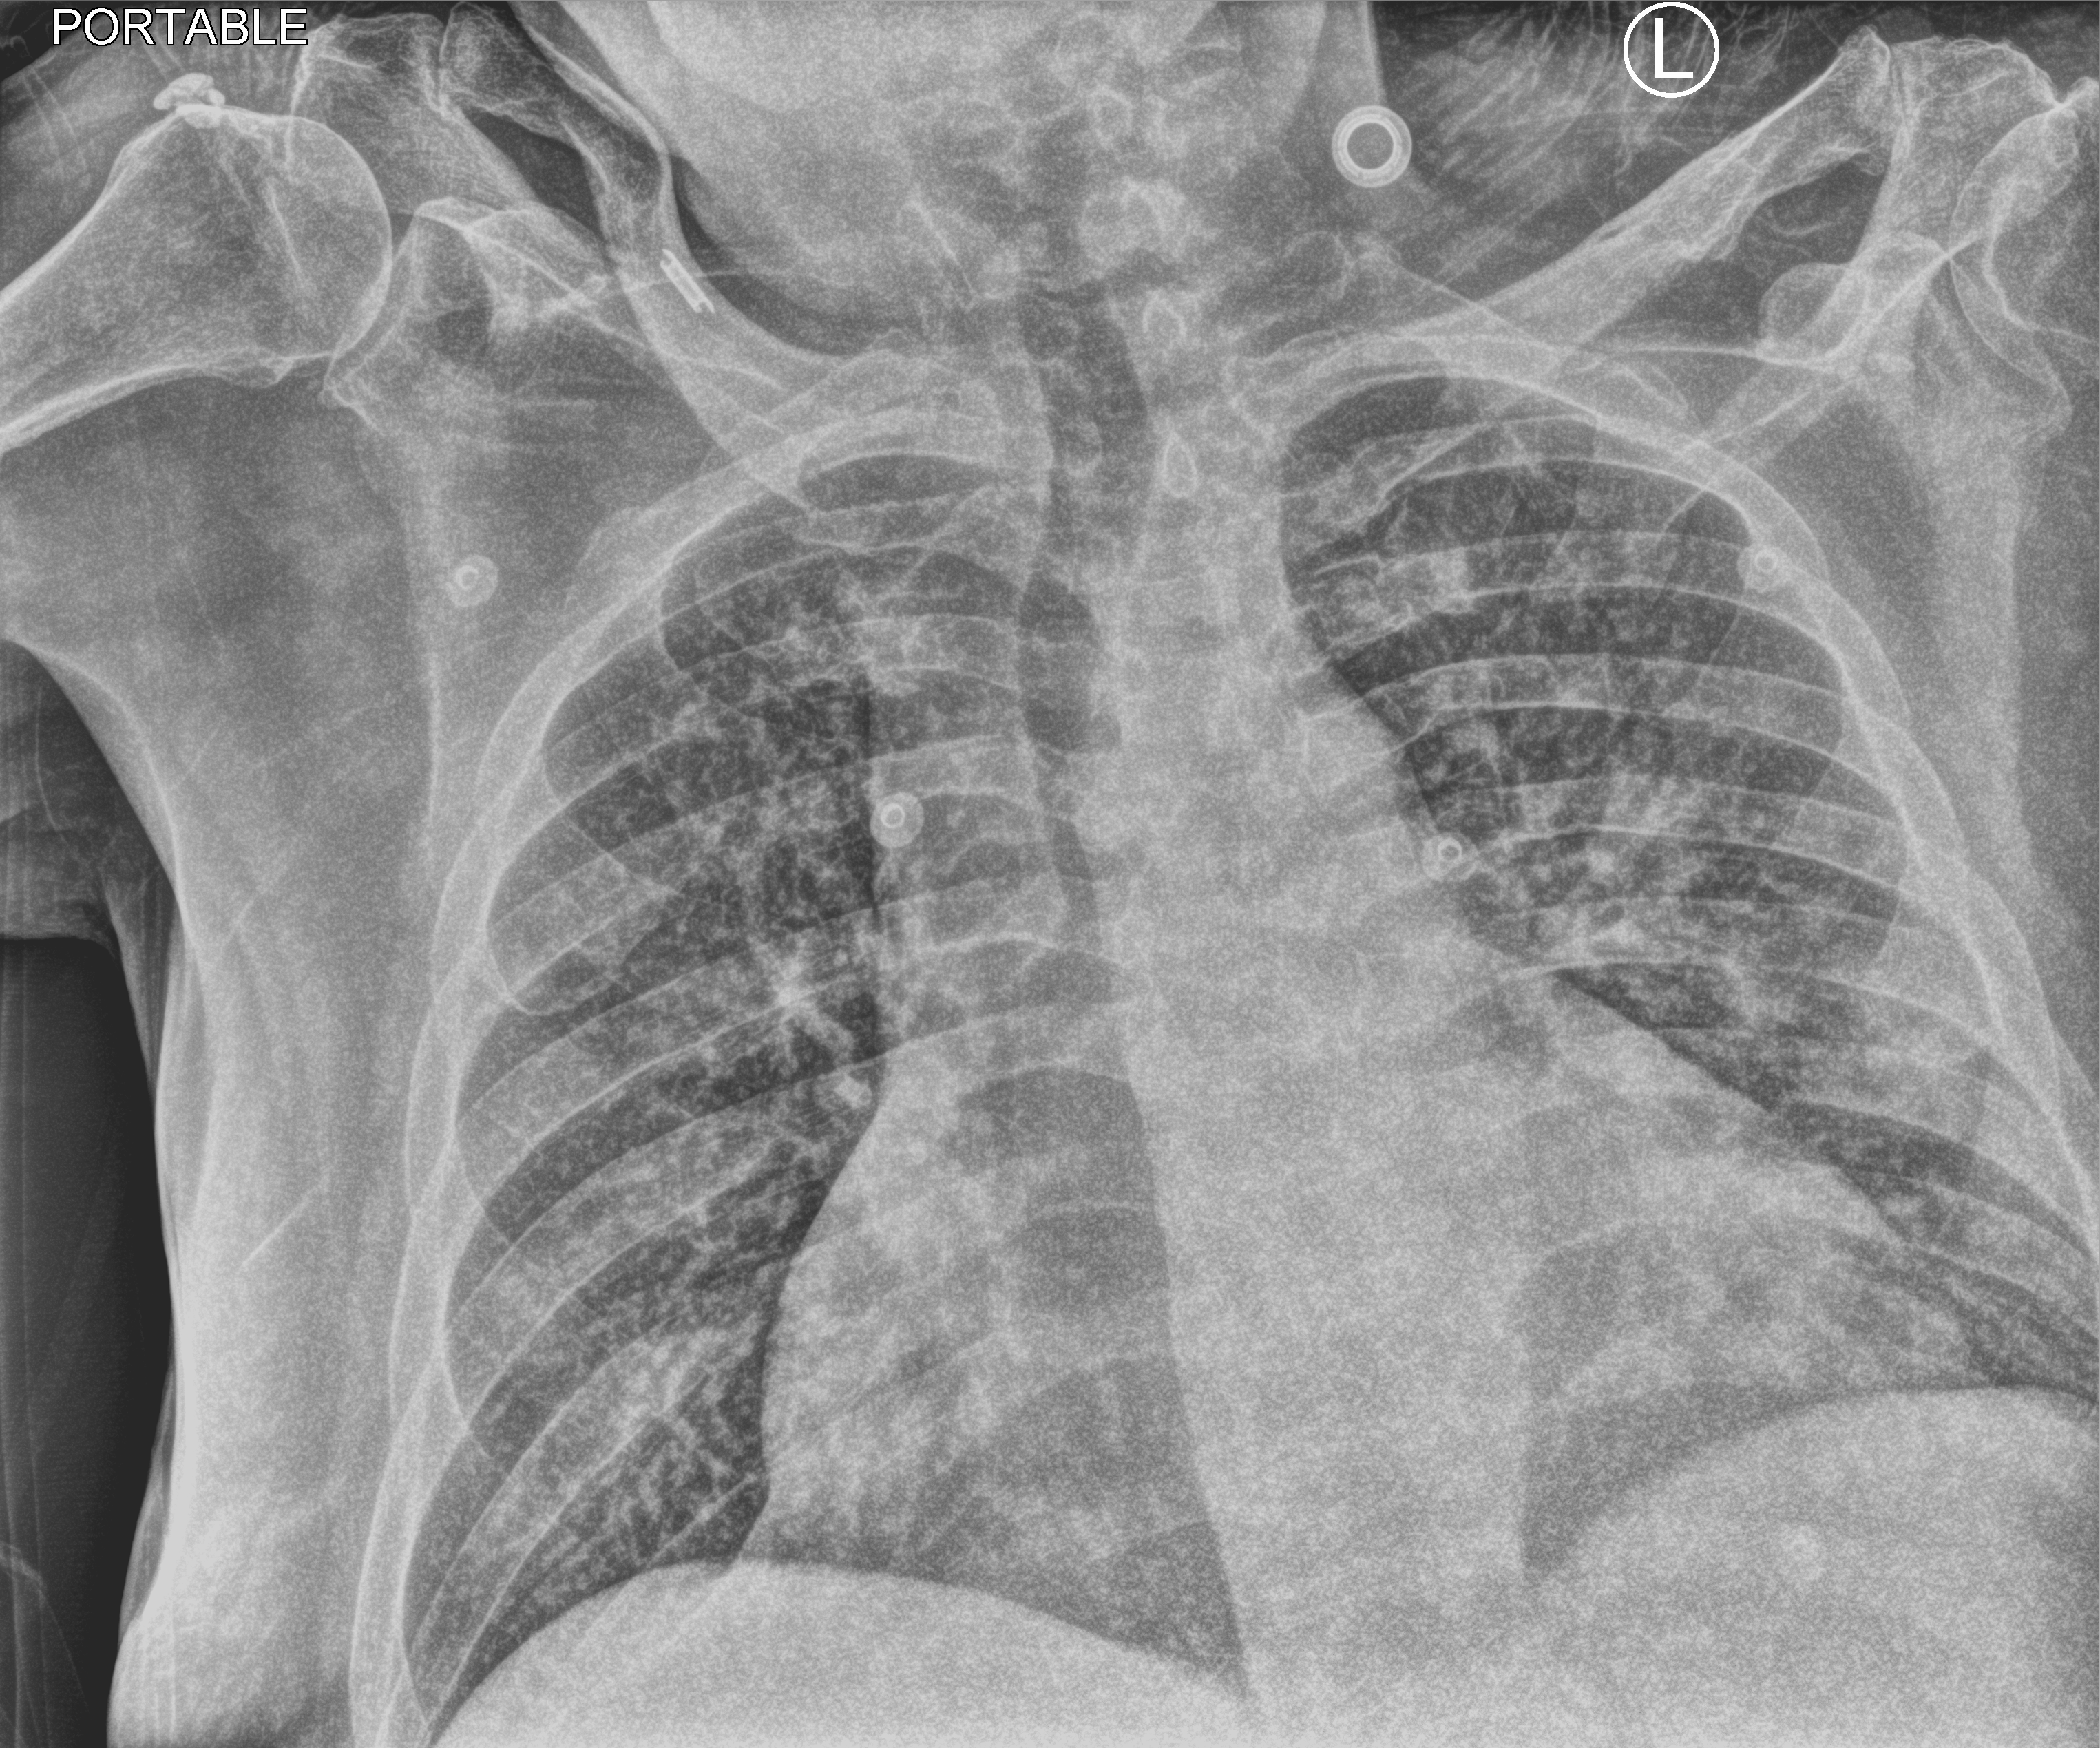
Chest X-ray (portable); anteroposterior (AP) projection. Male patient hospitalised with COVID-19, age 18–59 years.
From the hospital-stay record, not from the radiograph (when in the stay this image was taken is not recorded): mechanically ventilated during this hospital stay: no; admitted to intensive care during this hospital stay: no; length of hospital stay: 6 days.